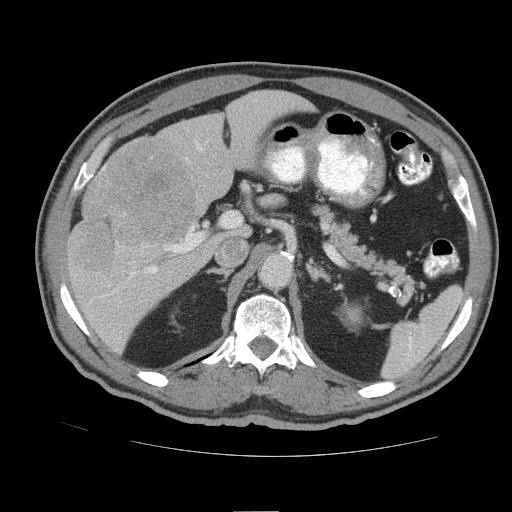
Contrast-enhanced abdominal CT (liver protocol), one axial slice; slice 53 of 105 in the series (ordered by position); soft-tissue window (W 400 / L 40 HU); 2.5 mm slice thickness; 512 × 512 image matrix, field of view 380 × 380 mm. From the clinical record (not read from this slice): diagnosis: hepatocellular carcinoma (patient treated with transarterial chemoembolisation; whether this scan precedes or follows treatment is not stated here); TNM stage (as recorded): Stage-IIIB; Child-Pugh class: A; tumour nodularity: multinodular.
Structures marked on this image (semi-automatic segmentation, software-assisted and operator-edited):
- liver parenchyma outside the tumour (the mass and vessels are separate outlines, so this box may not span the whole liver): bounding box (x1, y1, x2, y2) in pixels: (66, 90, 314, 353)
- mass: (72, 140, 199, 269)
- liver vessels: (102, 143, 203, 297)